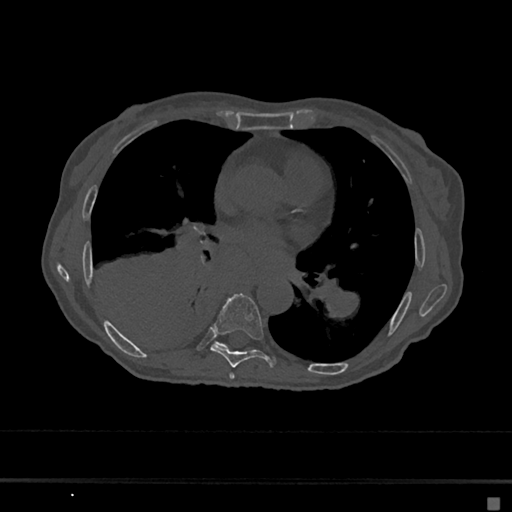
CT including the spine, one axial slice. Position 364 of 797 along the scan axis. 120 kVp. Bone window (W 1800 / L 400 HU). 0.5 mm slice thickness. 512 × 512 image matrix. Patient: female, 68 years. Case-level facts recorded for this patient, not image findings: primary cancer: renal.
Annotated regions visible in this slice (semi-automatically segmented with operator editing):
- T6 vertebra: box from (x=229, y=373) to (x=235, y=379) px
- T7 vertebra: (x=210, y=293)–(x=276, y=368)
- T8 vertebra: (x=216, y=342)–(x=227, y=348)